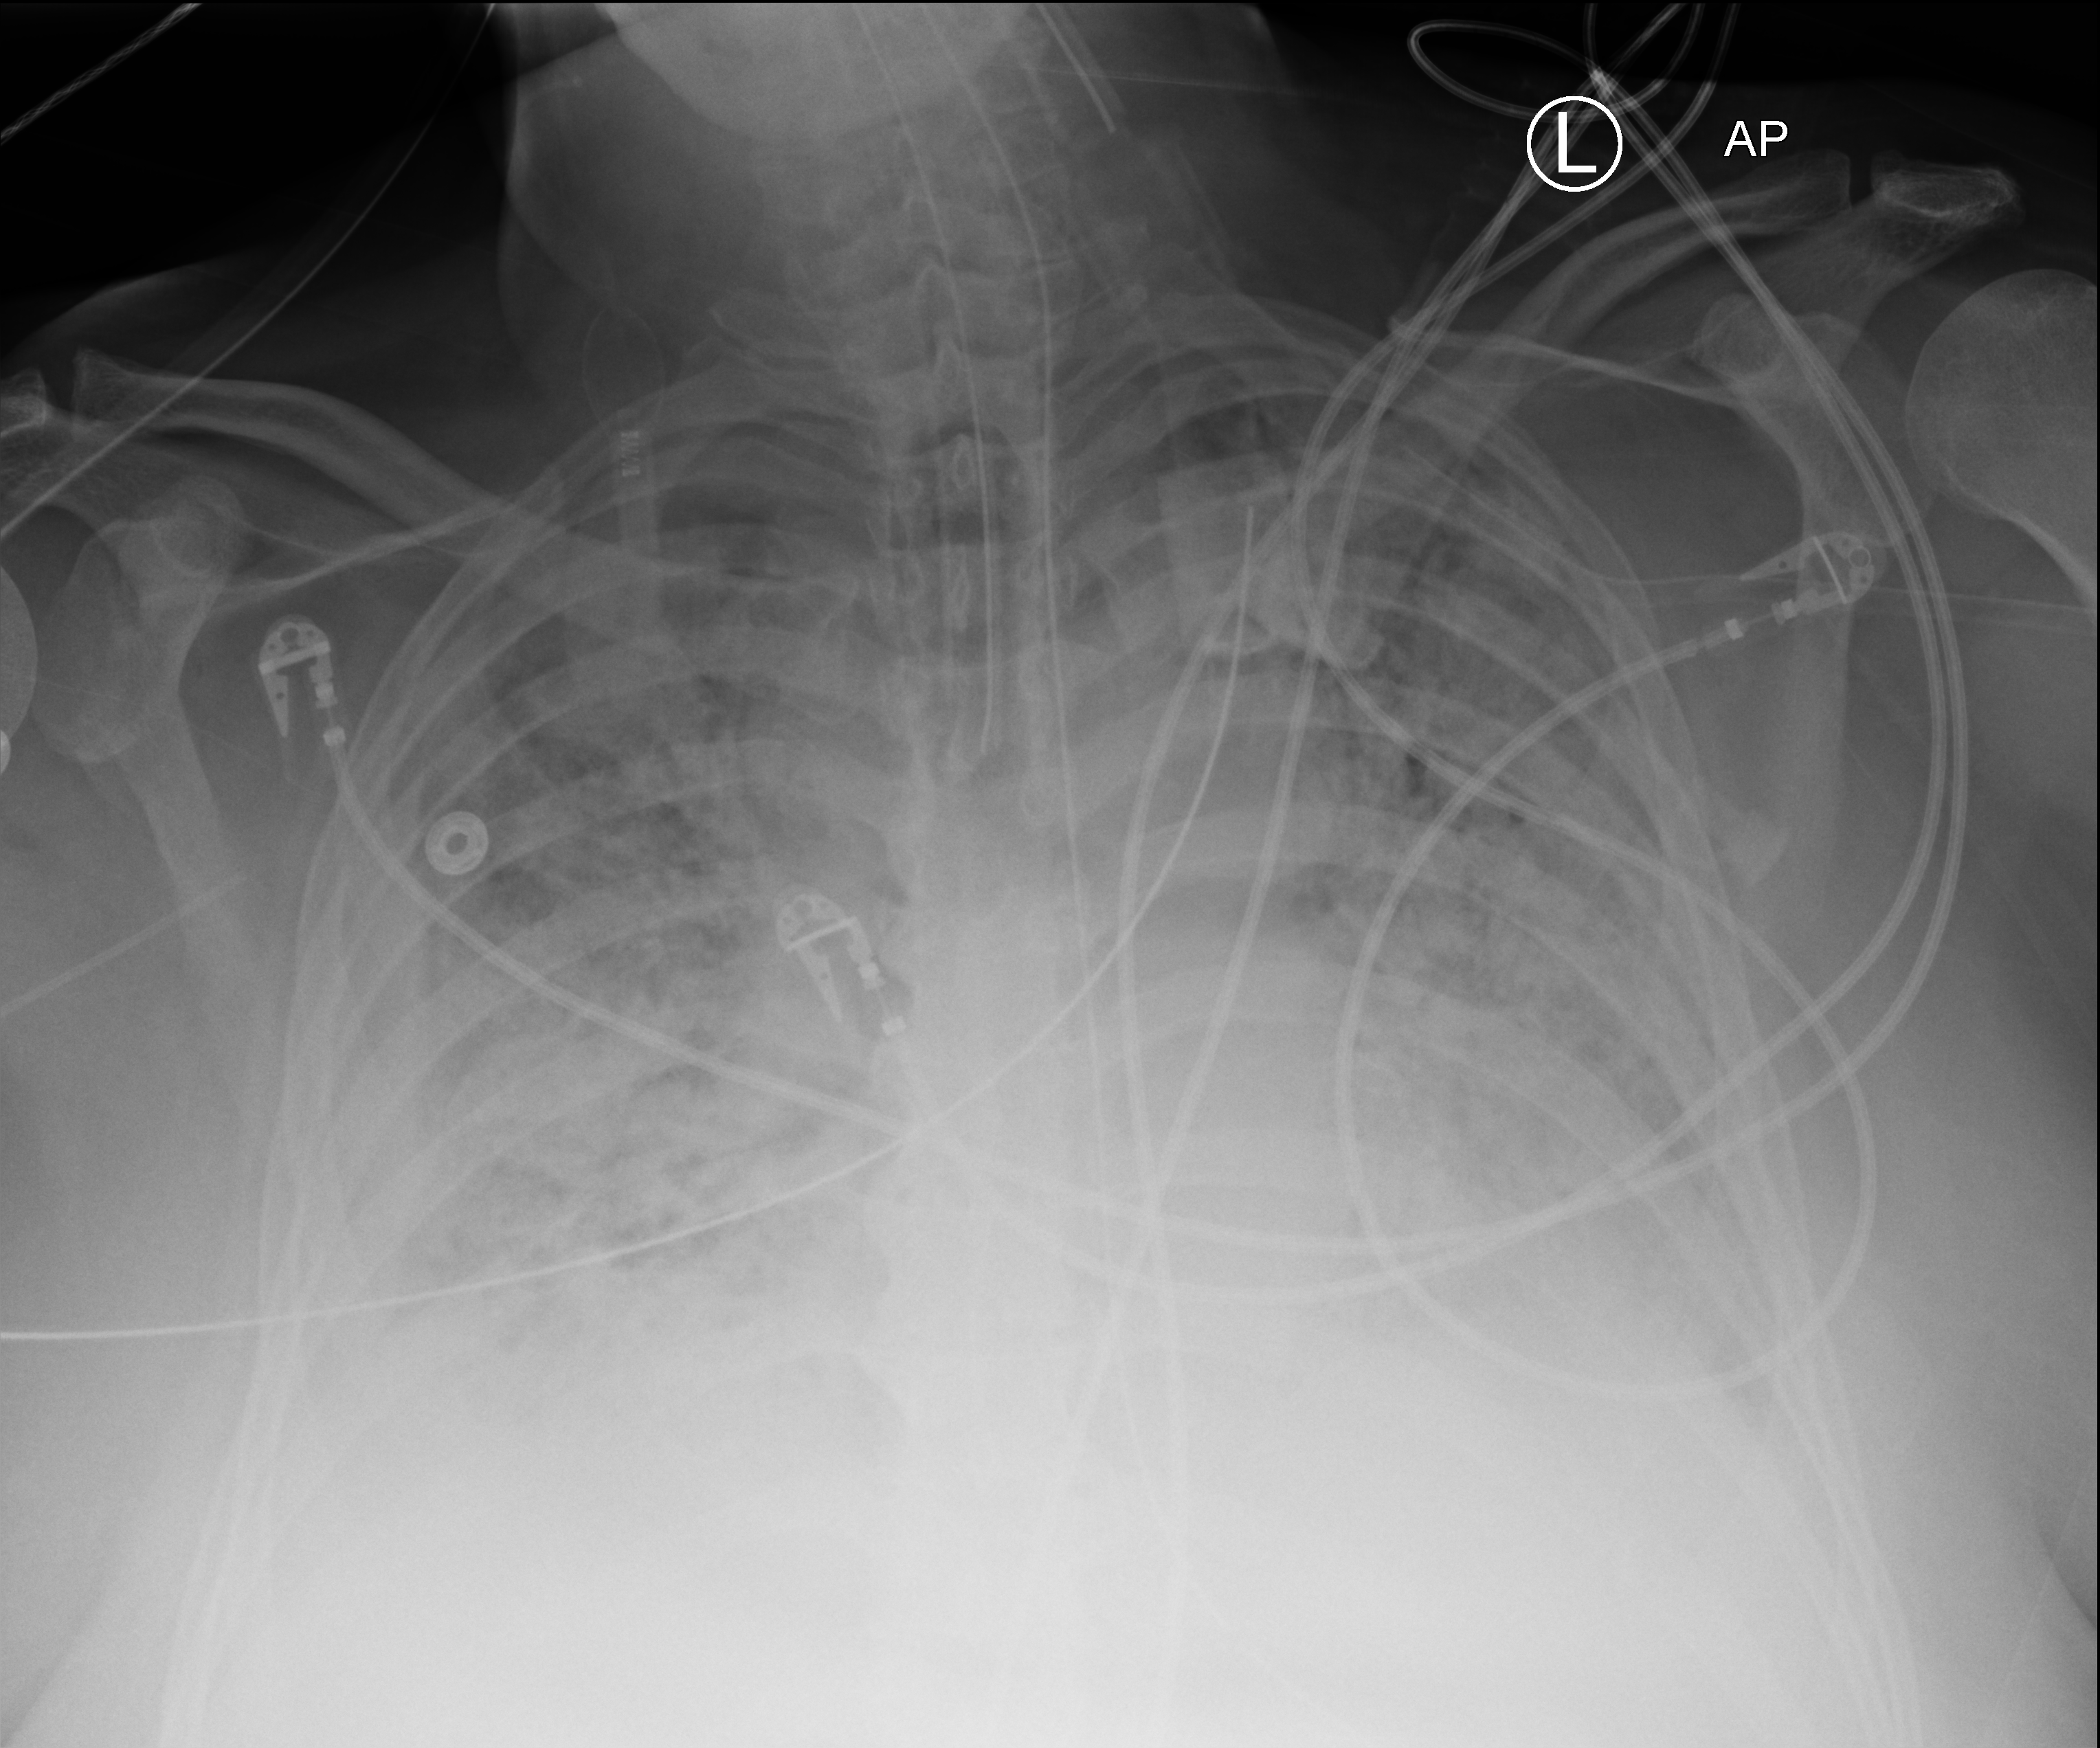
Chest X-ray (portable), anteroposterior (AP) projection. Patient hospitalised with COVID-19; male, aged 60–74 years.
Admission-level facts for this patient (not findings on this image; timing relative to this image not recorded): length of hospital stay: 40 days; COPD (admission record): no.